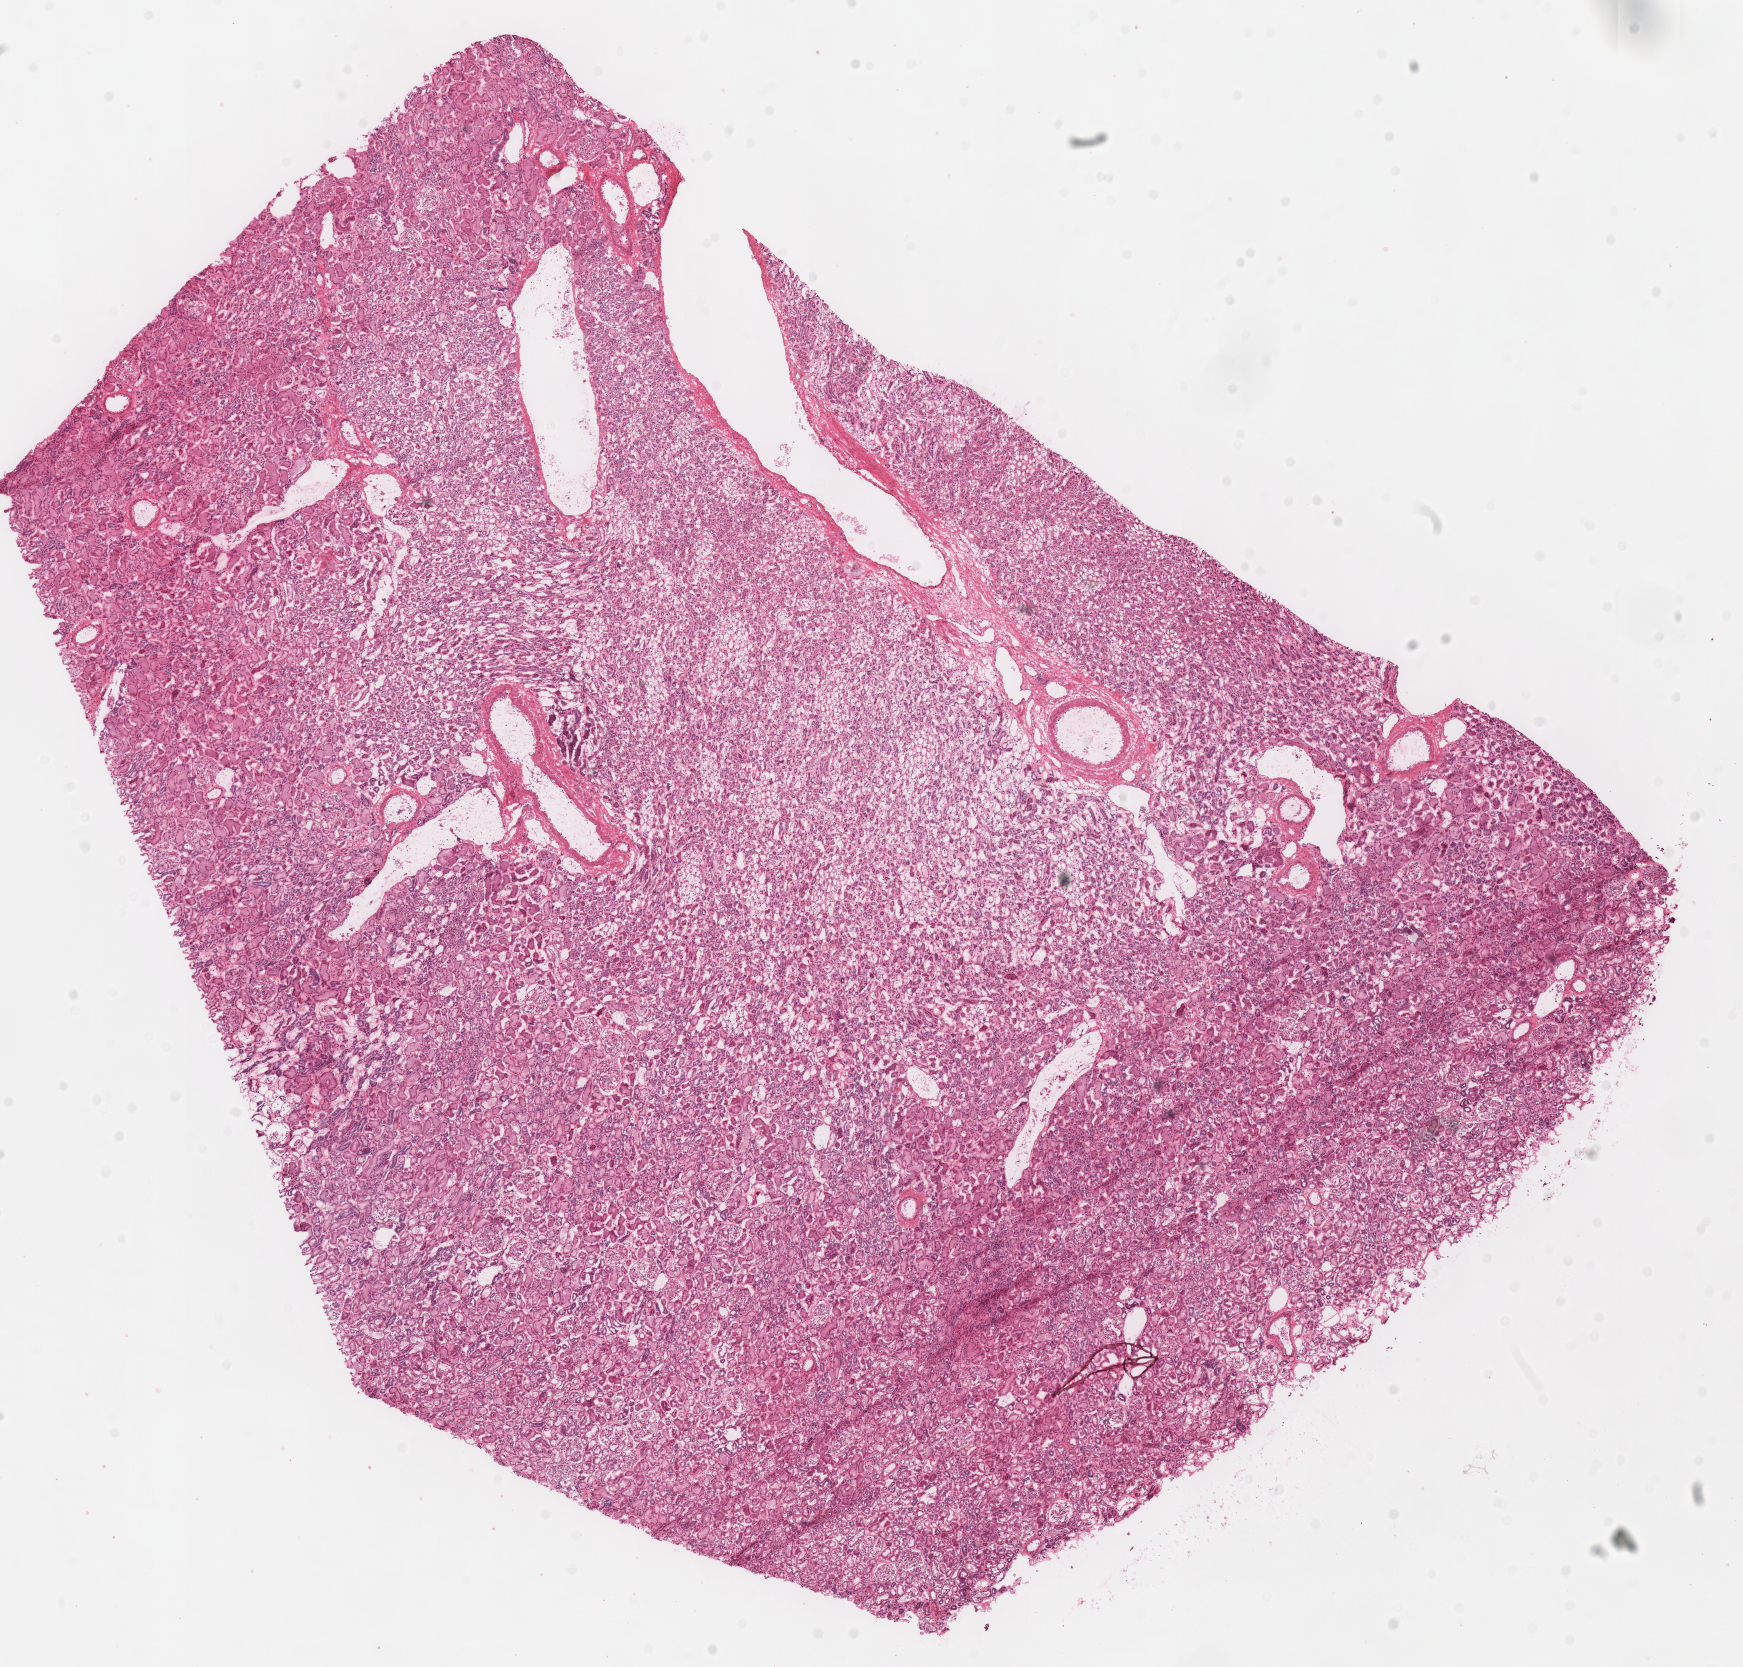
Whole-slide histology image, H&E, low-resolution overview of the scanned area, about 13.7 x 13.1 mm (acquisition: 40x scan), frozen section from the top of the tissue portion, solid tissue normal (non-tumour tissue) sample from the kidney. Patient: male, age at initial diagnosis 26 years.
• this section: solid tissue normal (non-tumour) sample from the same patient
• patient diagnosis: Renal cell carcinoma, chromophobe type